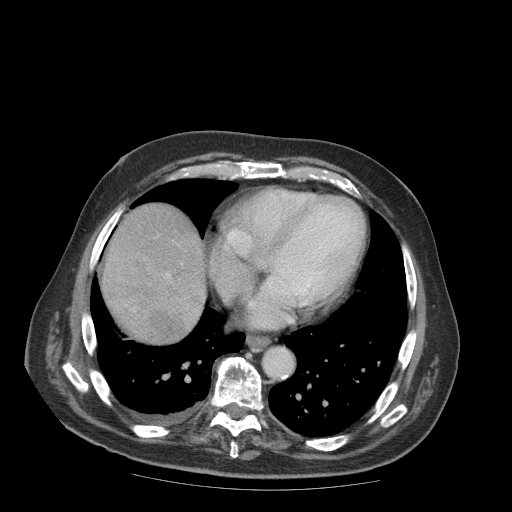
Contrast-enhanced abdominal CT (liver protocol), one axial slice. Slice 87 of 99 in the series (ordered by position). Soft-tissue window (W 400 / L 40 HU). 2.5 mm slice thickness. 512 × 512 image matrix. Case-level facts recorded for this patient, not image findings: diagnosis: hepatocellular carcinoma (patient treated with transarterial chemoembolisation; whether this scan precedes or follows treatment is not stated here); TNM stage (as recorded): Stage-IIIB; Child-Pugh class: A; tumour differentiation: well differentiated.
Outlined on this slice (semi-automatically segmented with operator editing):
- abdominal aorta: bounding box <262,347,294,378> (left, top, right, bottom; pixels)
- liver parenchyma outside the tumour (the mass and vessels are separate outlines, so this box may not span the whole liver): <100,204,206,342>
- mass: <101,238,201,343>
- liver vessels: <166,274,170,277>